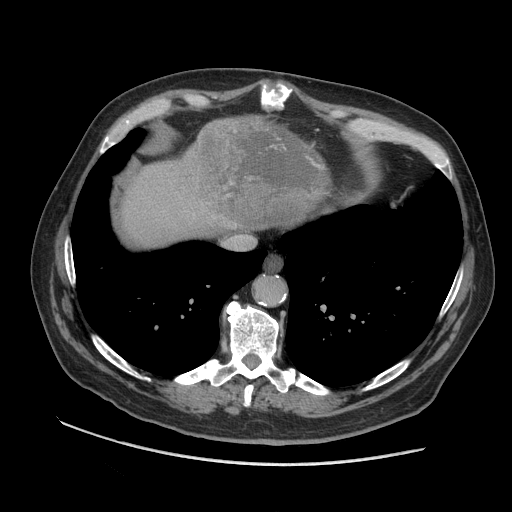
Contrast-enhanced abdominal CT (liver protocol), one axial slice. Position 90 of 109 along the scan axis. Reconstruction kernel STANDARD. 140 kVp. Soft-tissue window (W 400 / L 40 HU). 2.5 mm slice thickness. 512 × 512 image matrix, field of view 420 × 420 mm. Case-level facts recorded for this patient, not image findings: diagnosis: hepatocellular carcinoma (patient treated with transarterial chemoembolisation; whether this scan precedes or follows treatment is not stated here); TNM stage (as recorded): Stage-I; Child-Pugh class: A; tumour nodularity: uninodular.
Annotated regions visible in this slice (semi-automatically segmented with operator editing):
- liver parenchyma outside the tumour (the mass and vessels are separate outlines, so this box may not span the whole liver): bounding box [x1, y1, x2, y2] px = [120, 116, 261, 246]
- mass: [198, 116, 334, 233]